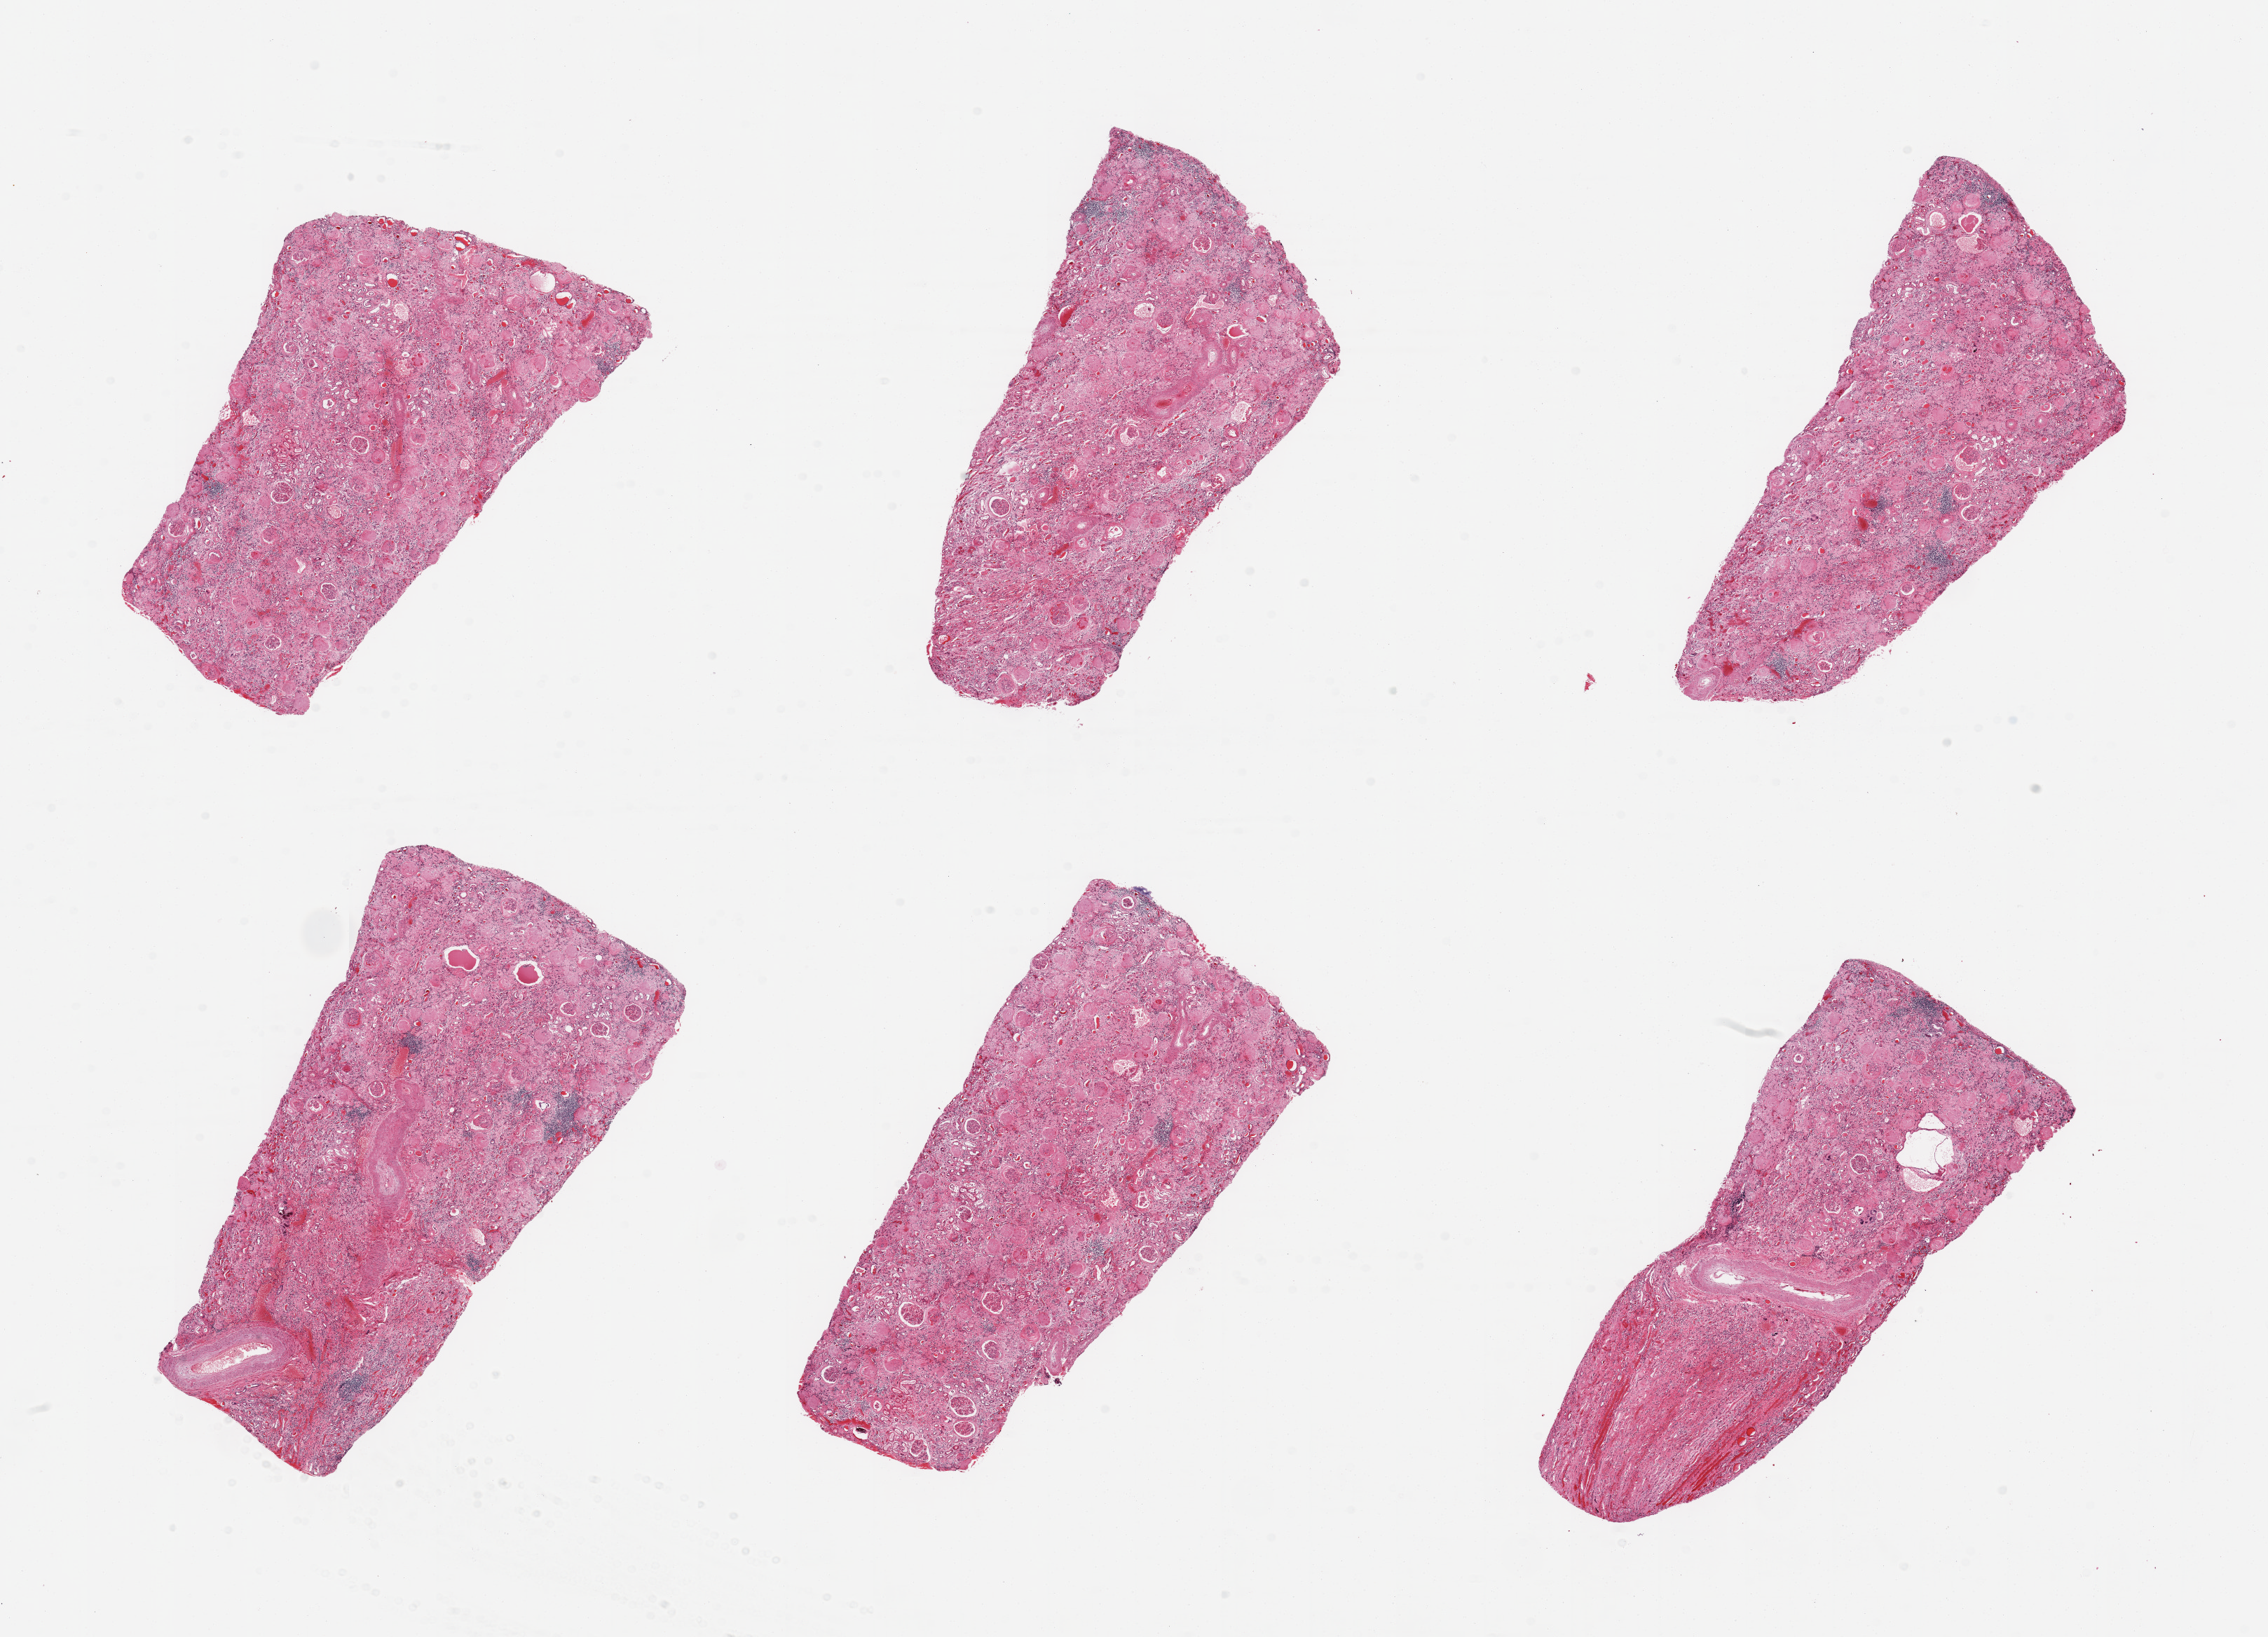
Hematoxylin and eosin (H&E) whole-slide image, brightfield — a low-resolution overview of the entire scanned area, about 25.6 x 18.5 mm. PAXgene-fixed, paraffin-embedded tissue. Section of renal cortex (target tissue). Donor tissue sample. Male donor.
Reviewer comment on this tissue sample: 6 pieces; mild to moderate autolysis; advanced arterio and arteriolonephrosclerosis and diabetic glomerulopathy; majority of glomeruli hyalinized; chronic interstitial inflammation; end stage renal disease.